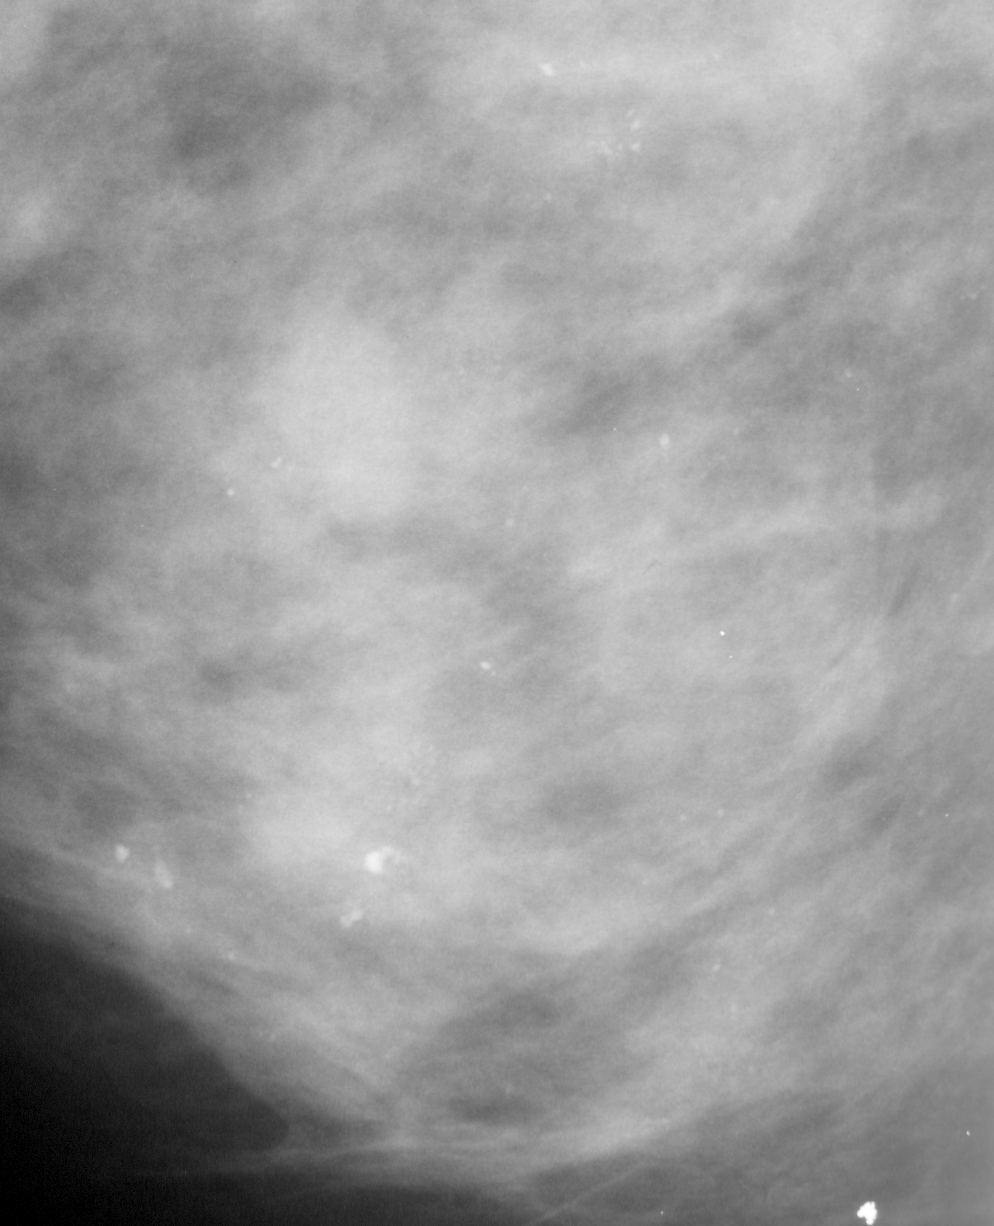
Cropped region of a digitized screen-film mammogram centred on a radiologist-marked abnormality; left breast; MLO view; BI-RADS breast density category 3 (scale 1–4).
Calcifications, morphology pleomorphic, distribution segmental; BI-RADS assessment category 4; pathology (as recorded): malignant.